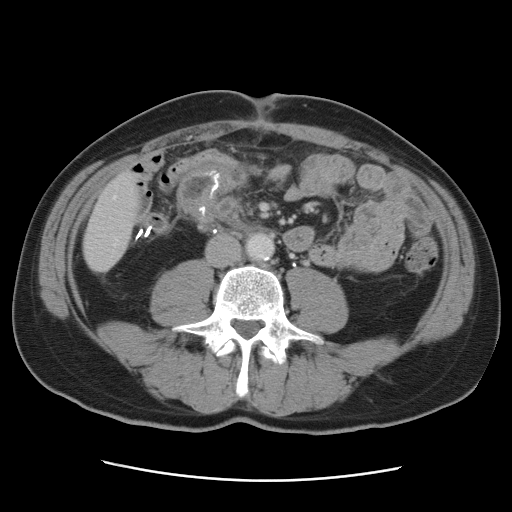
Contrast-enhanced abdominal CT, one axial slice; position 11 of 89 along the scan axis; intravenous contrast given; soft-tissue window (W 400 / L 40 HU); 5 mm slice thickness; 512 × 512 image matrix. Male patient, age 59 years. Case-level facts recorded for this patient, not image findings: diagnosis: colorectal cancer liver metastases, imaged before liver resection; multiple liver metastases: yes; largest metastasis: 0.6 cm; disease in both lobes: yes.
Annotated regions visible in this slice (manually delineated by an expert):
- hepatic veins: bounding box (x1, y1, x2, y2) in pixels: (113, 196, 118, 245)
- liver: (83, 174, 141, 271)
- planned liver remnant (the part of the liver to remain after resection): (84, 173, 141, 259)